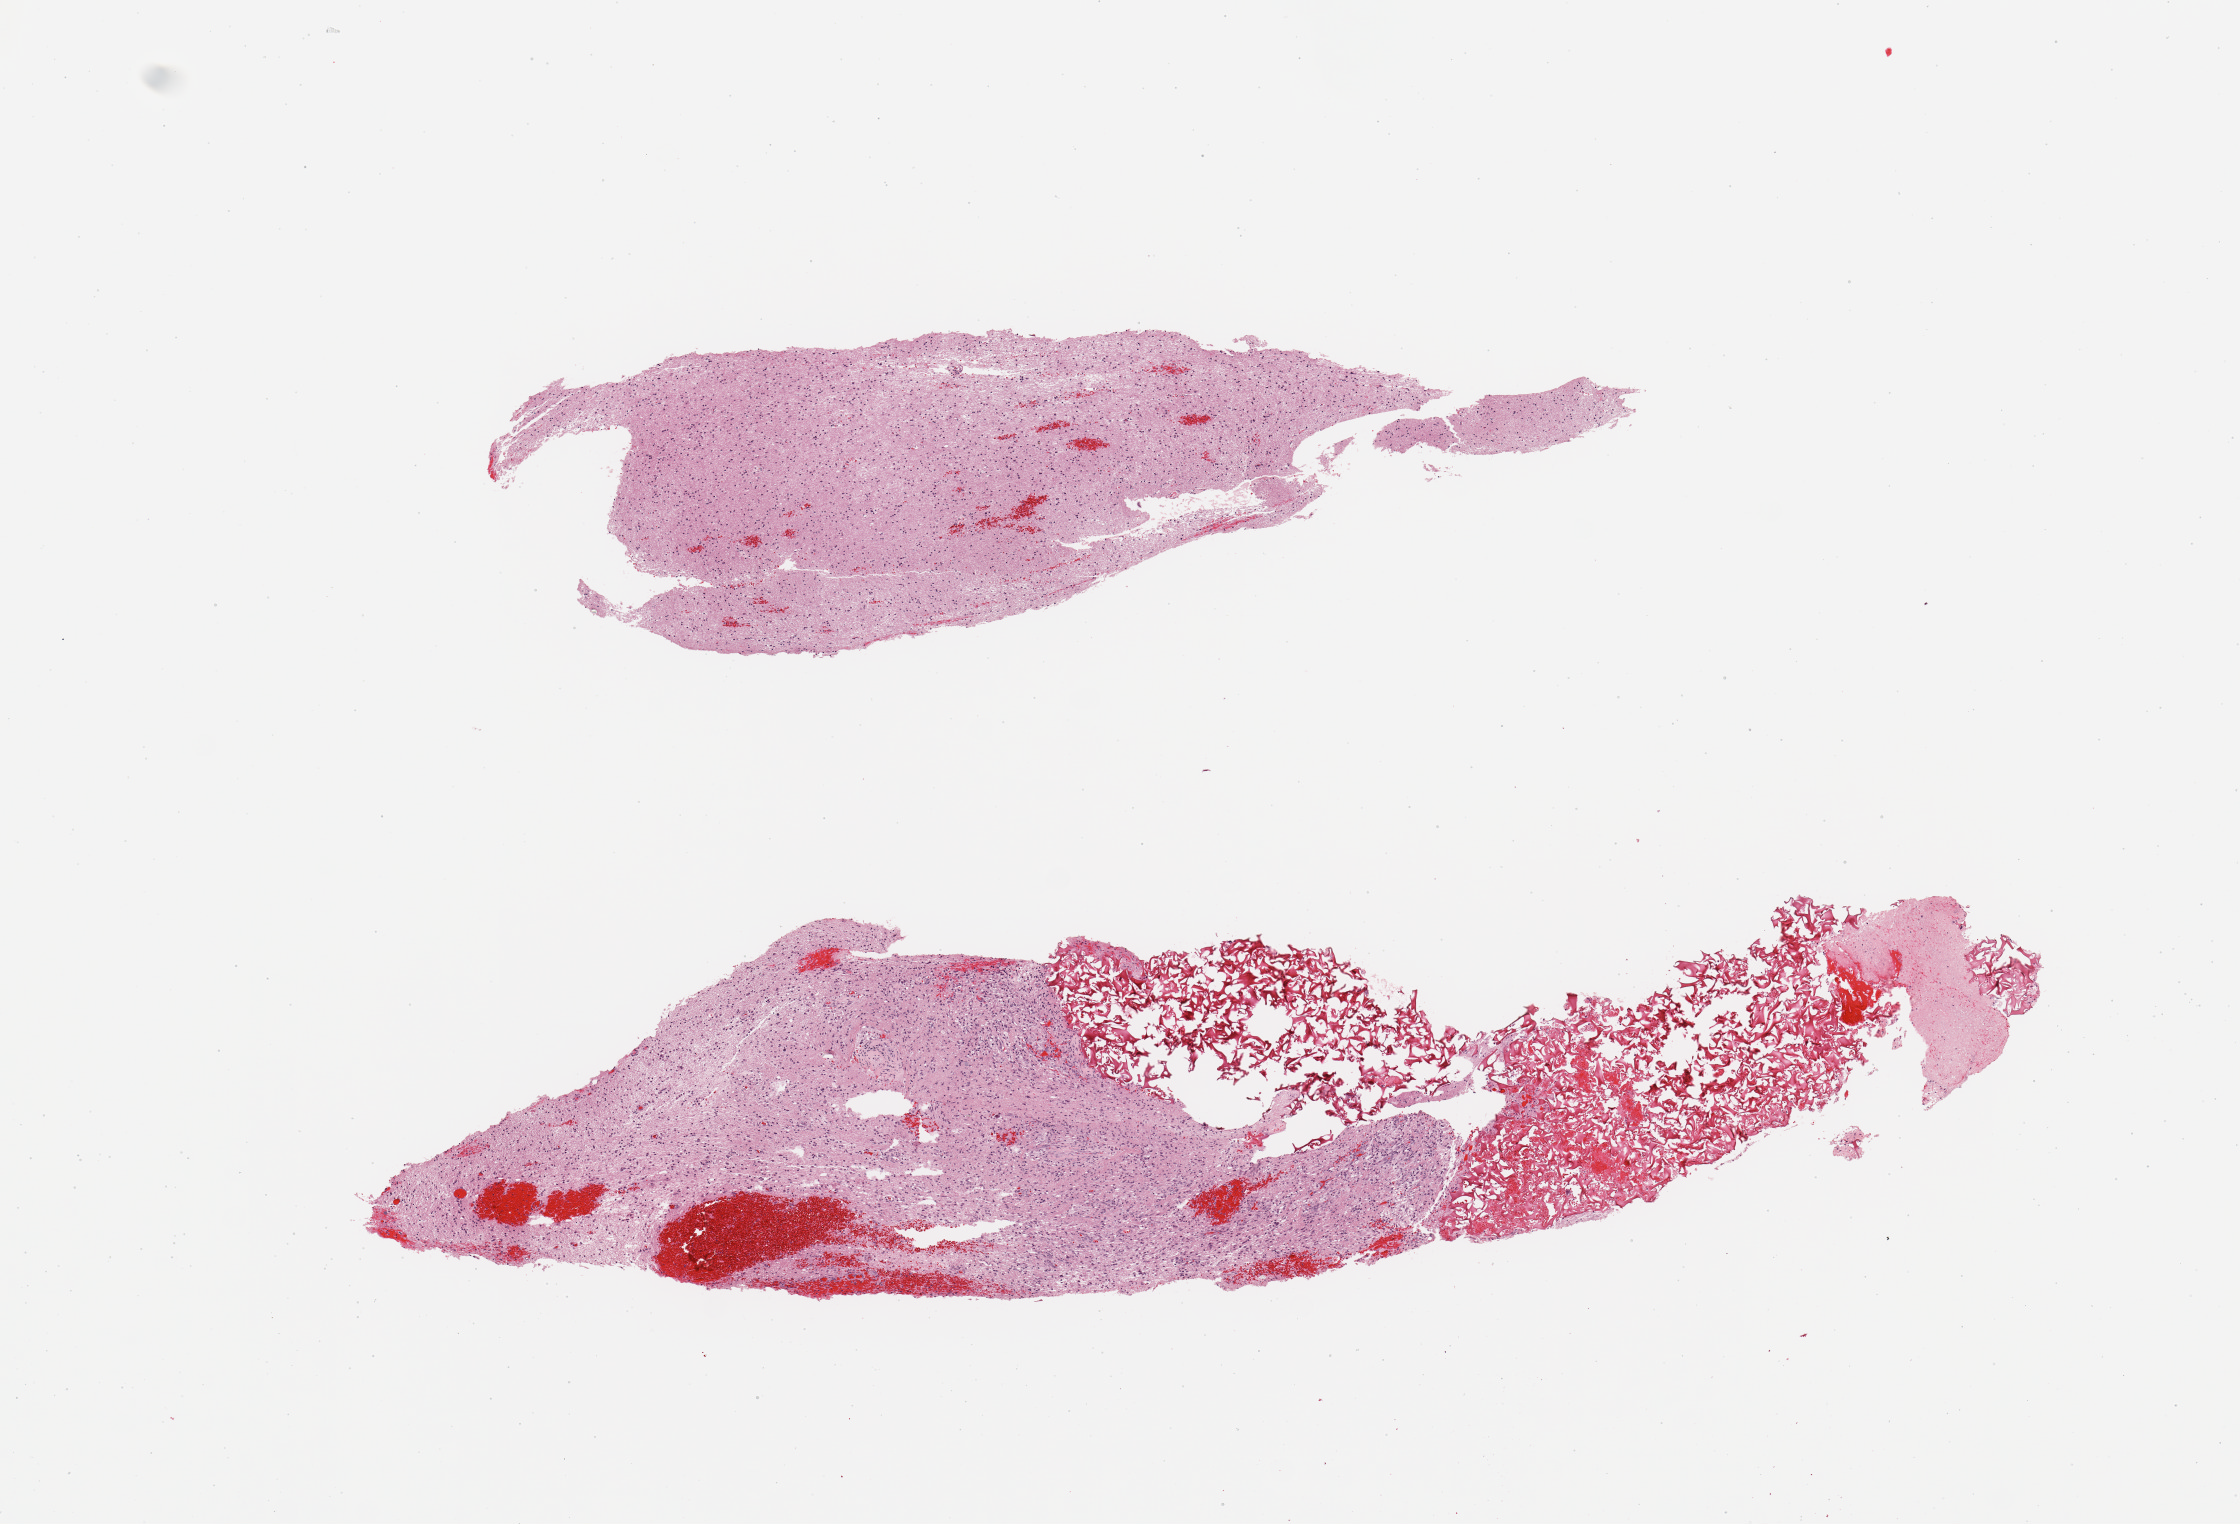
Digitized H&E tissue section (whole slide) — whole scanned area (about 8.9 x 6.0 mm) shown as a low-resolution overview. Tumour tissue sample, sampled site: brain. Patient: female, age 76 years. Composition of this section per pathologist review: tumour nuclei 60%, necrosis 10%.
Primary tumour site (as recorded): temporal lobe. Histologic diagnosis: Glioblastoma.